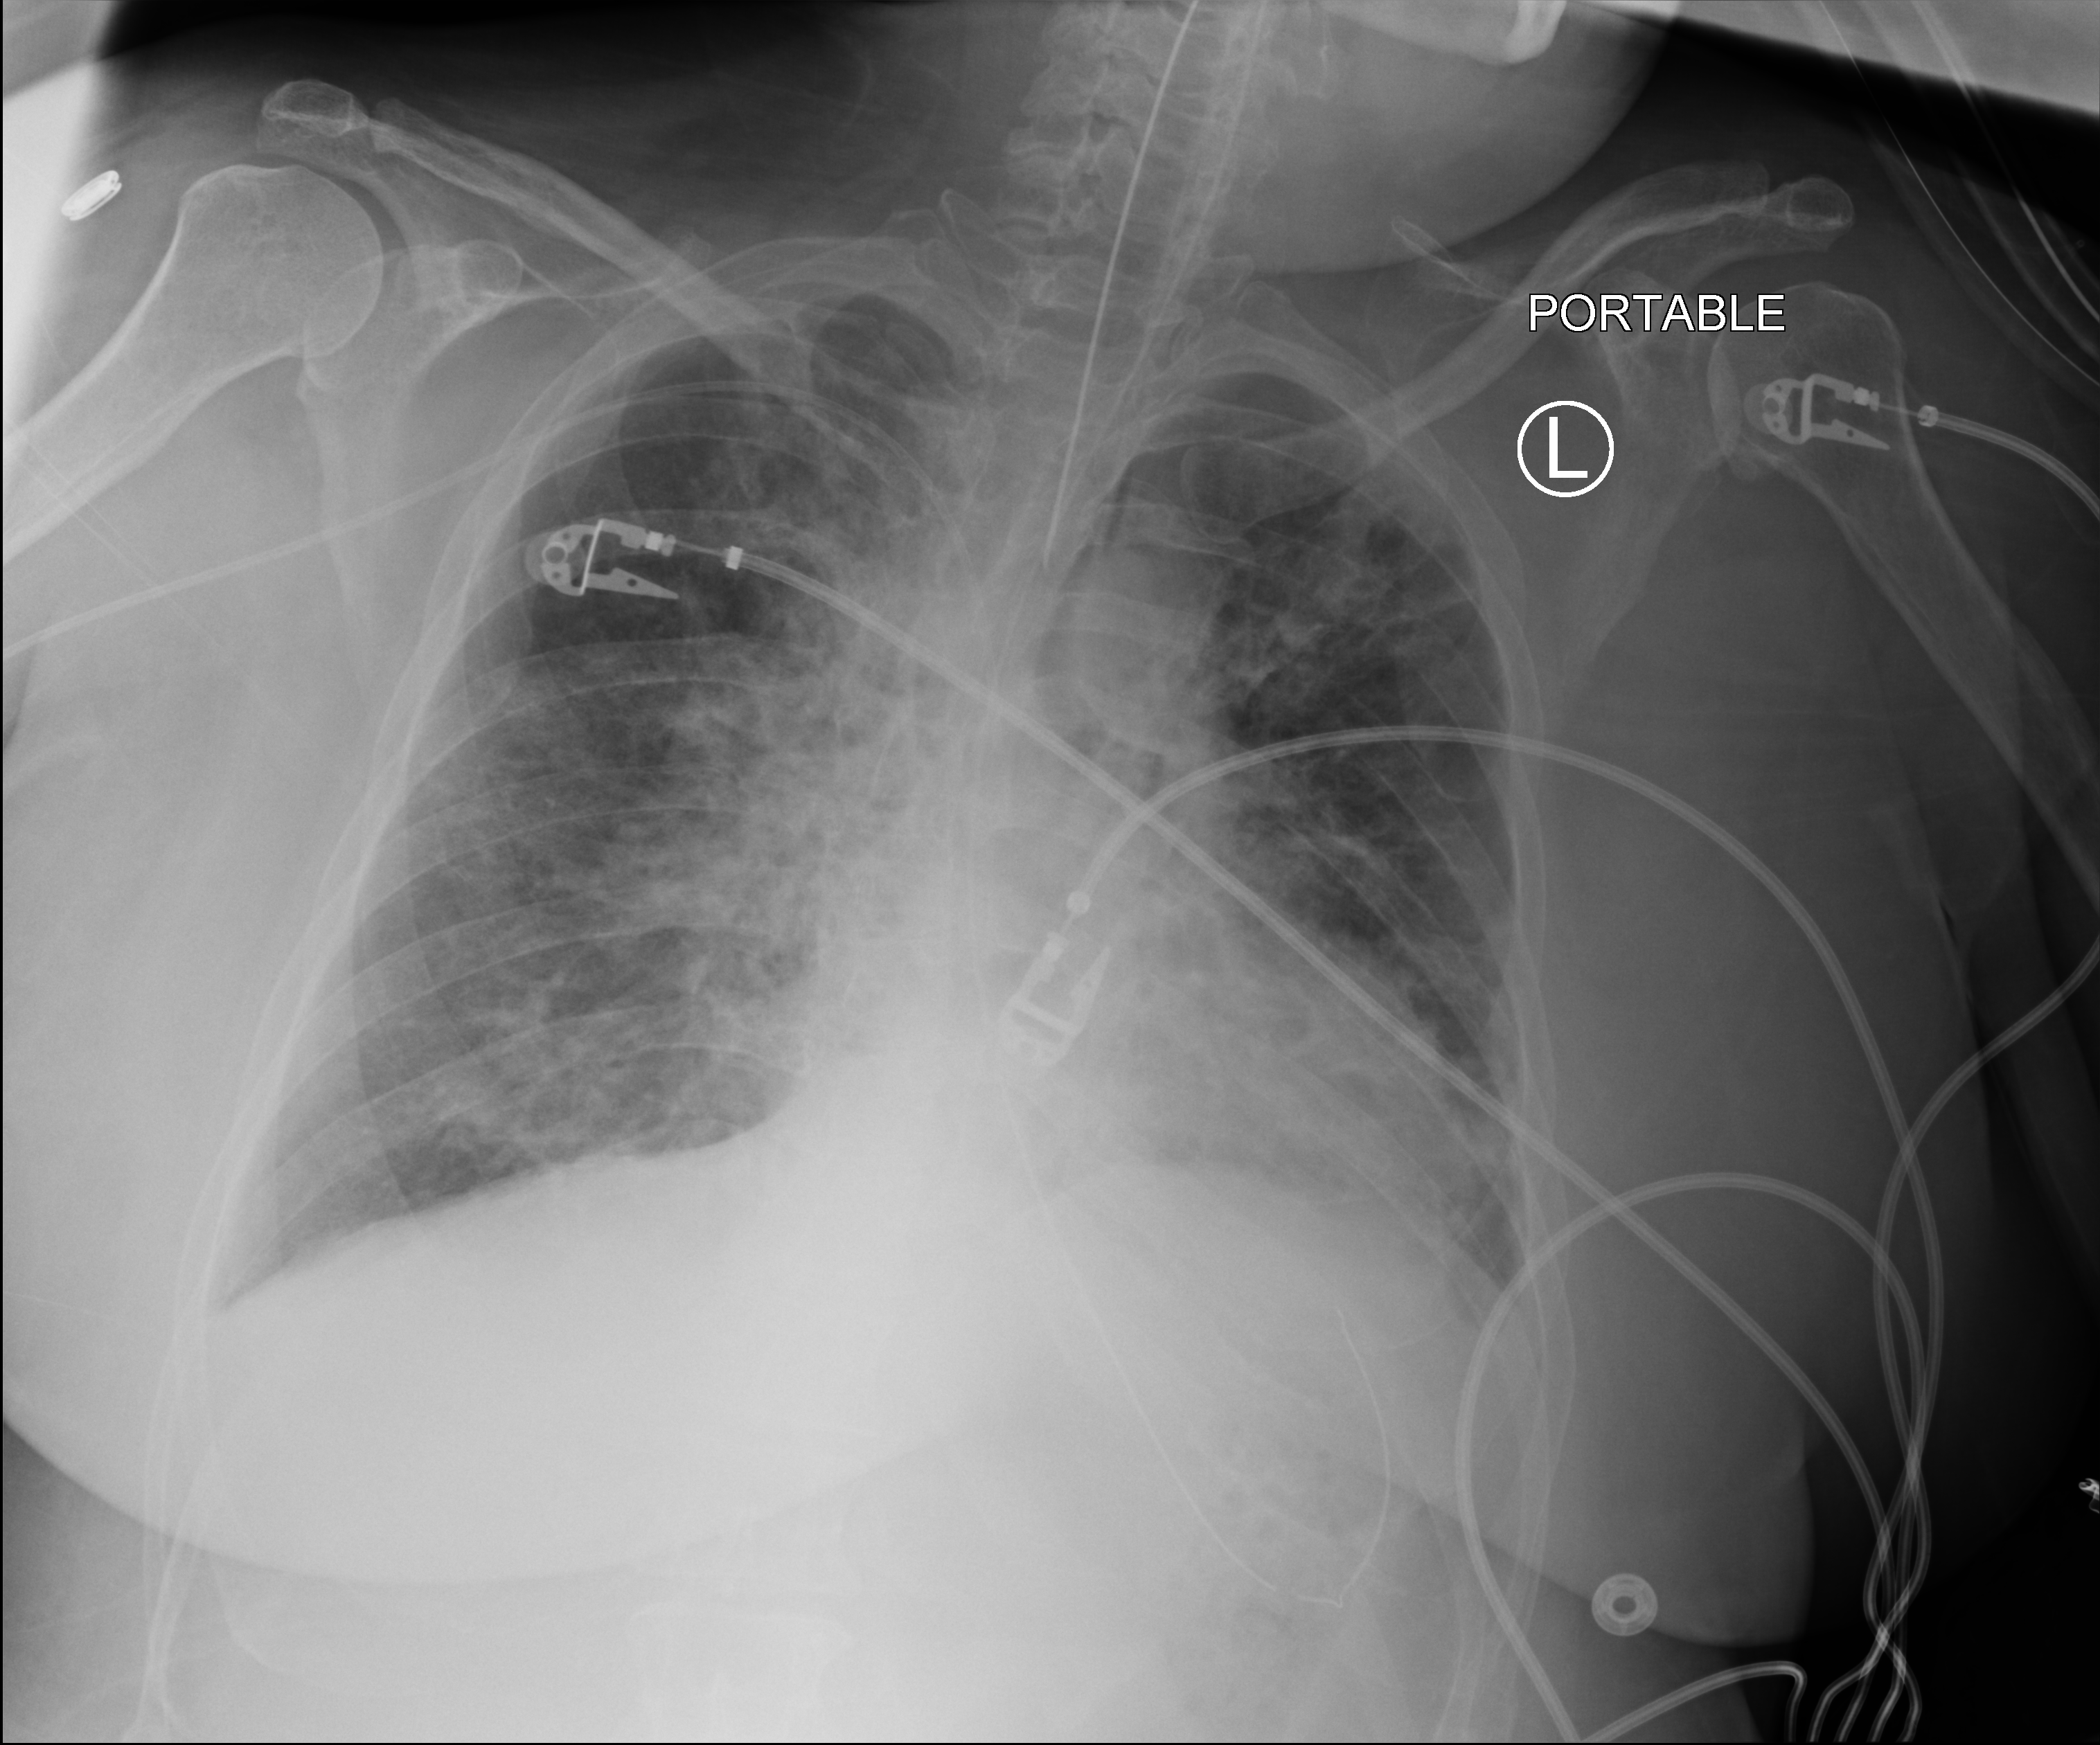
Bedside chest radiograph (computed radiography); anteroposterior (AP) projection. Adult patient hospitalised with COVID-19, age 18–59 years.
Hospital-stay facts (about this admission, not read from this image; timing relative to this image not recorded):
- length of hospital stay: 15 days
- admitted to intensive care during this hospital stay: yes